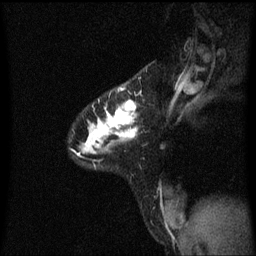
Breast MRI (dynamic contrast-enhanced), one sagittal slice; slice 46 of 60 in the series (ordered by position); dynamic contrast-enhanced series, image 2 of 3 at this slice position (ordered by acquisition); 1.5 T; TE 4.2 ms, TR 8.4 ms; 2 mm slice thickness; 256 × 256 image matrix. Female patient, age 32 years.
Structures marked on this image (semi-automatically segmented with operator editing):
- analysis volume of interest (the breast-tissue region the enhancement analysis was run in; not a lesion): bounding box [x1, y1, x2, y2] px = [80, 82, 138, 167]
- tumour enhancement mask (voxels above the 70 % enhancement threshold inside the analysis volume of interest): [80, 88, 138, 155]